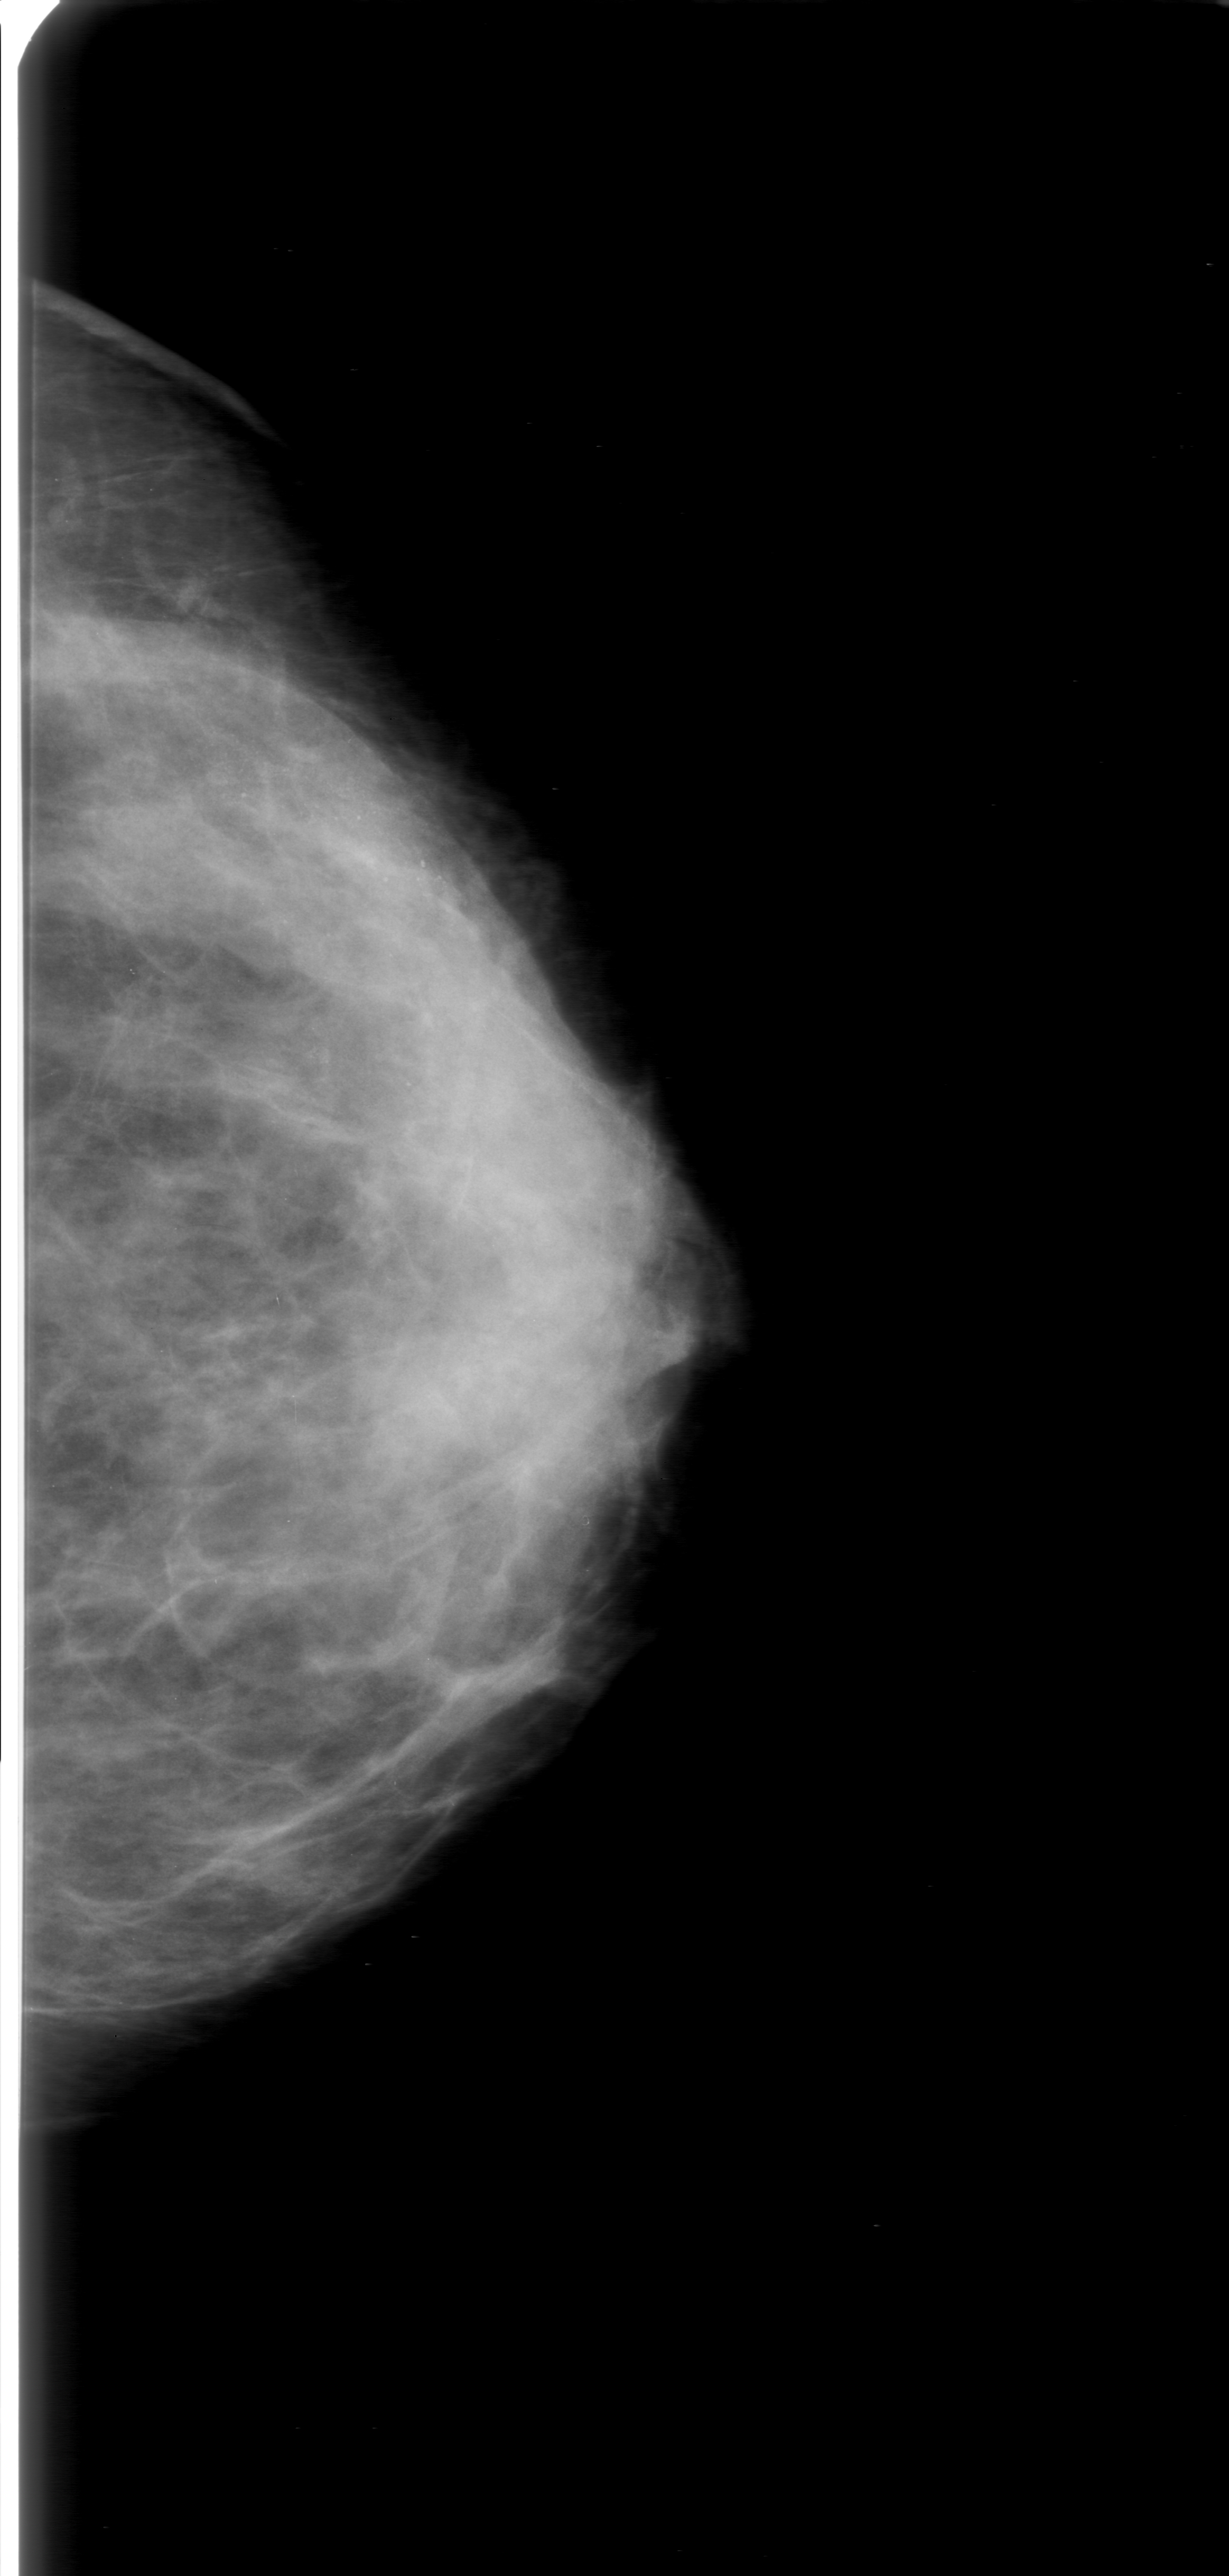
Digitized screen-film mammogram; left breast; CC view; BI-RADS breast density category 3 (scale 1–4).
- Marked abnormality: calcifications, morphology amorphous, distribution segmental; BI-RADS assessment category 0 (incomplete: needs additional imaging); pathology result (as recorded, not read from the image): benign.